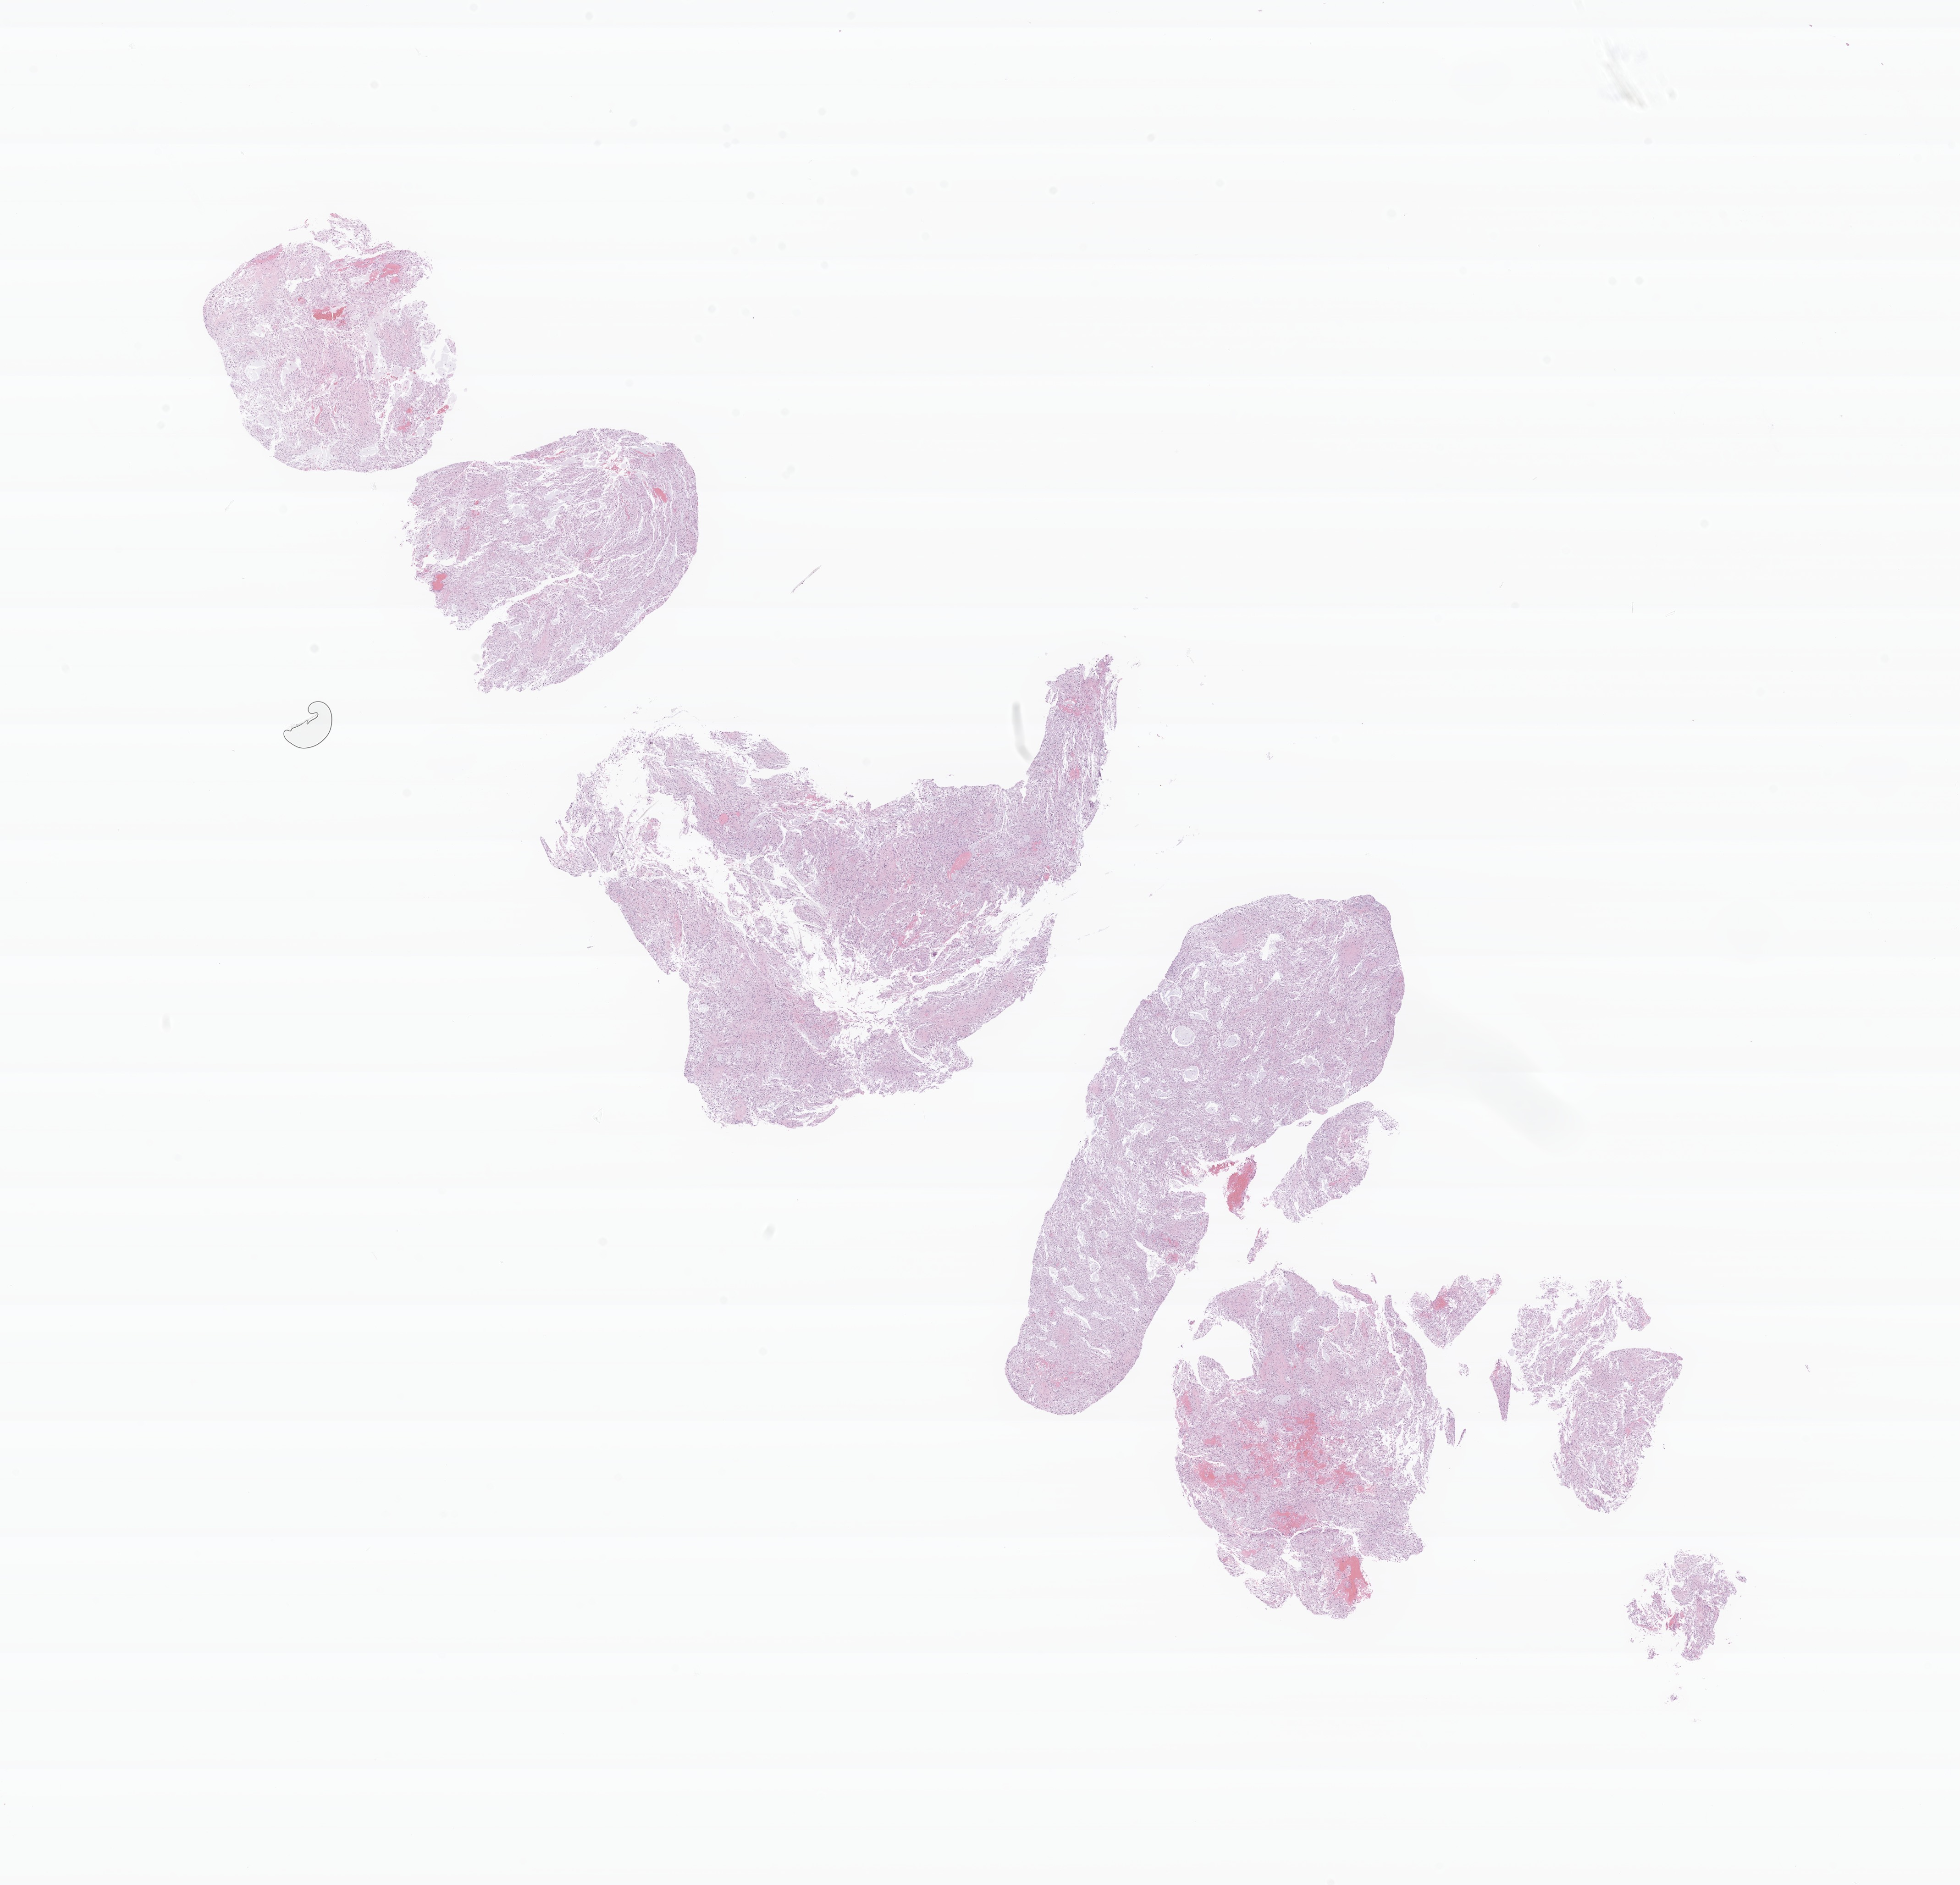
Whole-slide image, H&E stain of tumor tissue from the brain, whole scanned area (about 18.0 x 17.3 mm) shown as a low-resolution overview; FFPE section. Patient female; age 44 months (3 years 8 months).
• diagnosis (ICD-O-3 morphology term): Pilocytic astrocytoma